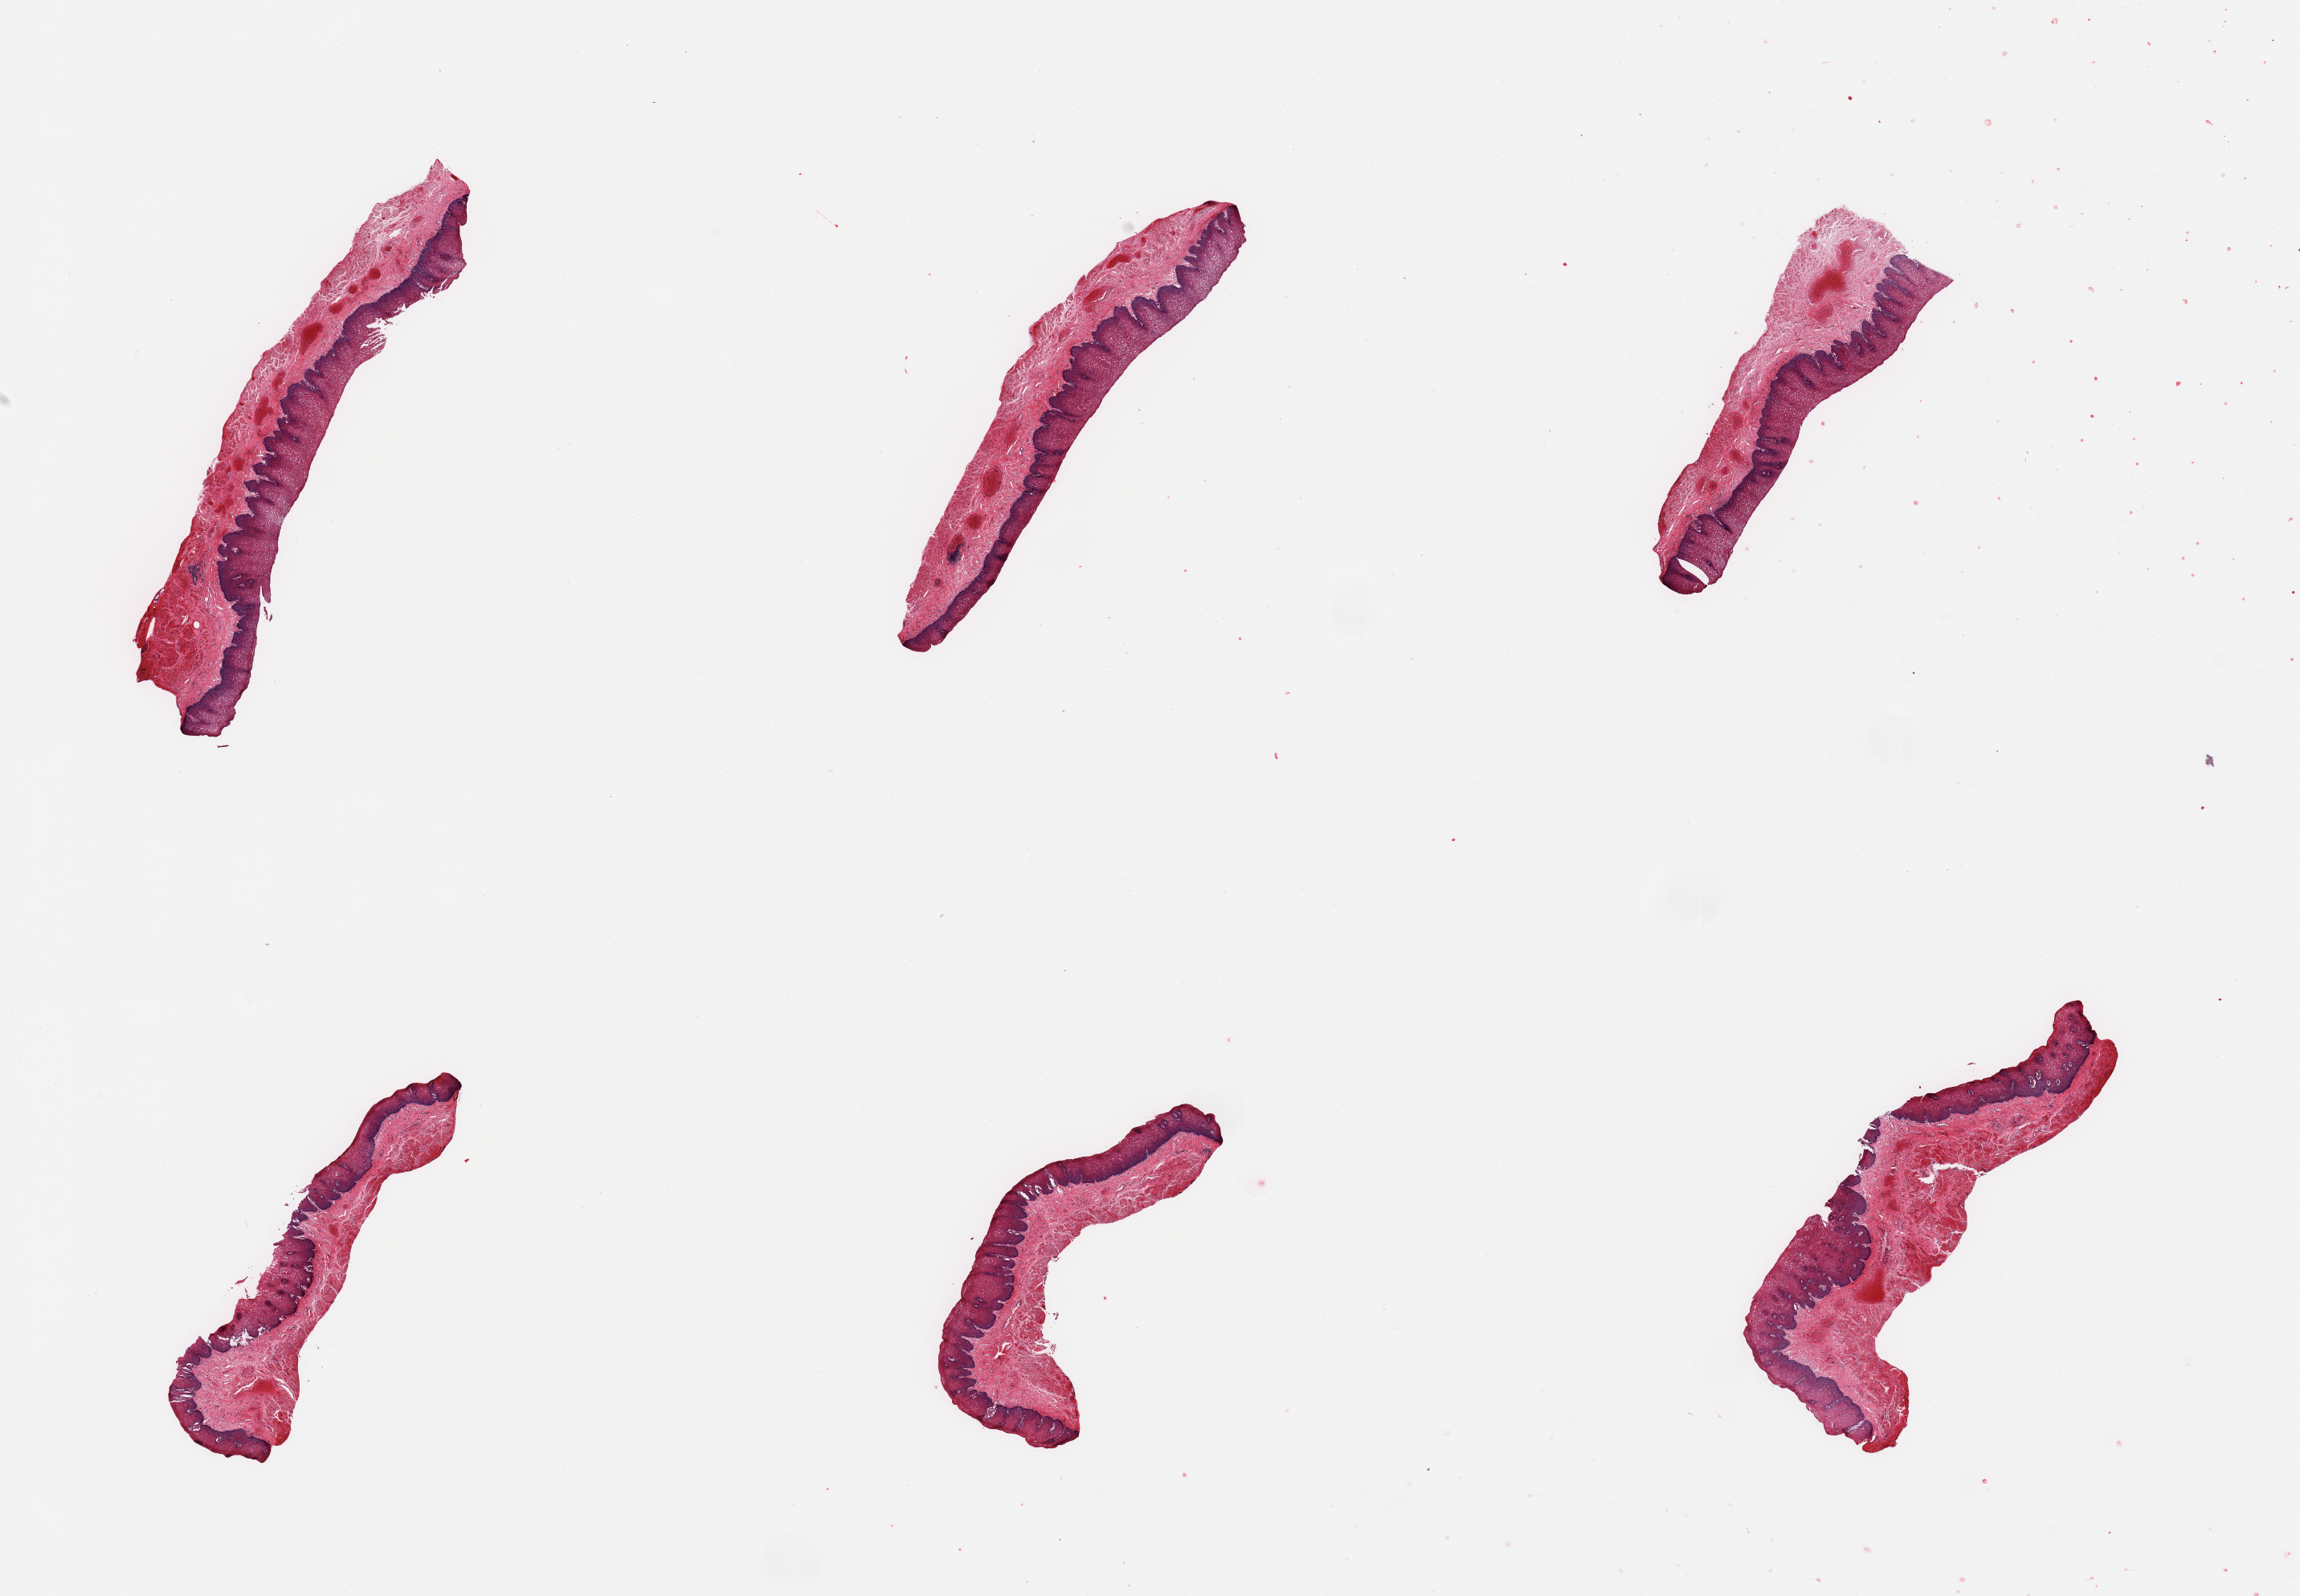
H&E whole-slide image, brightfield, a low-resolution overview of the entire scanned area, about 22.6 x 15.7 mm. PAXgene-fixed paraffin-embedded (PFPE) section. Section of esophageal mucous membrane (target tissue). Donor tissue sample. Donor: male.
* pathologist's review note for this sample: 6 pieces; congestion; ~0.28mm thick squamous epithelium